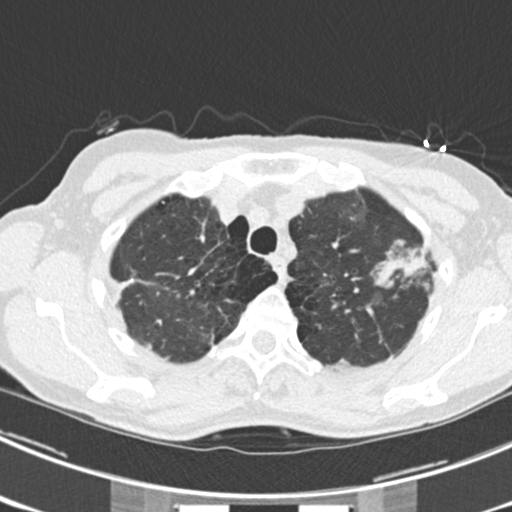
Low-dose screening chest CT, axial slice. Third annual screen. Lung window (W 1500 / L -600 HU). 512 × 512 image matrix. Female, age 63 years at enrolment. Current smoker at enrolment.
Expert reader's lesion annotation, bounding box <375,233,444,295> (left, top, right, bottom; pixels). The screening reader recorded 9 non-calcified nodules or masses ≥4 mm on this exam (left upper lobe, right upper lobe, left upper lobe, left lower lobe, right middle lobe, left lower lobe, left lower lobe, right lower lobe, right lower lobe); which of them this box marks is not recorded. Official screen result: positive, other. Lung cancer was diagnosed 15 days after this screen: bronchiolo-alveolar adenocarcinoma, NOS, right upper lobe, right middle lobe, right lower lobe, left upper lobe, left lower lobe, moderately differentiated (G2), stage IV (AJCC 6th edition).